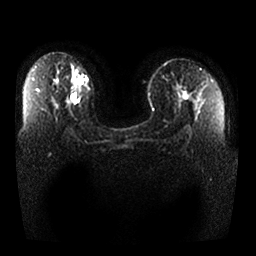
Breast MRI, one axial slice. Position 18 of 25 along the scan axis. Diffusion-weighted series; image 2 of 4 stored at this slice position (different b-values; order by instance number). 1.5 T. 4 mm slice thickness. 256 × 256 image matrix. Female patient.
Structures marked on this image (outlined manually by an expert reader):
- tumour on diffusion-weighted imaging: box from (x=78, y=79) to (x=85, y=85) px